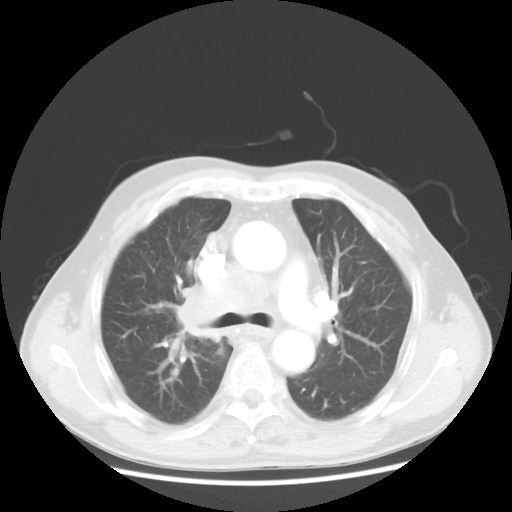
Chest CT, one axial slice; position 79 of 124 along the scan axis; 100 kVp; lung window (W 1500 / L -600 HU); 5 mm slice thickness; 512 × 512 image matrix, field of view 382 × 382 mm. Male patient, age 64 years. From the clinical record (not read from this slice): clinical TNM (as recorded): T3 N3 M0; histopathological grade: G3.
Outlined on this slice (rectangle marked by the reading radiologist):
- lung tumour (recorded histology: small cell carcinoma): bounding box [x1, y1, x2, y2] px = [177, 274, 225, 359]